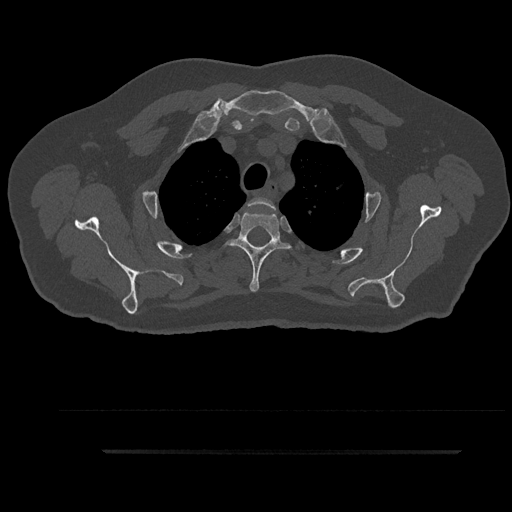
CT including the spine, one axial slice. Slice 718 of 797 in the series (ordered by position). Reconstruction kernel Br40s/3. 120 kVp. Bone window (W 1800 / L 400 HU). 0.5 mm slice thickness. 512 × 512 image matrix. Male patient, age 63 years. Case-level facts recorded for this patient, not image findings: primary cancer: renal; vertebrae with lytic lesions (as recorded): T8.
Annotated regions visible in this slice (semi-automatically segmented with operator editing):
- T2 vertebra: box from (x=248, y=197) to (x=275, y=209) px
- T3 vertebra: (x=227, y=211)–(x=290, y=292)